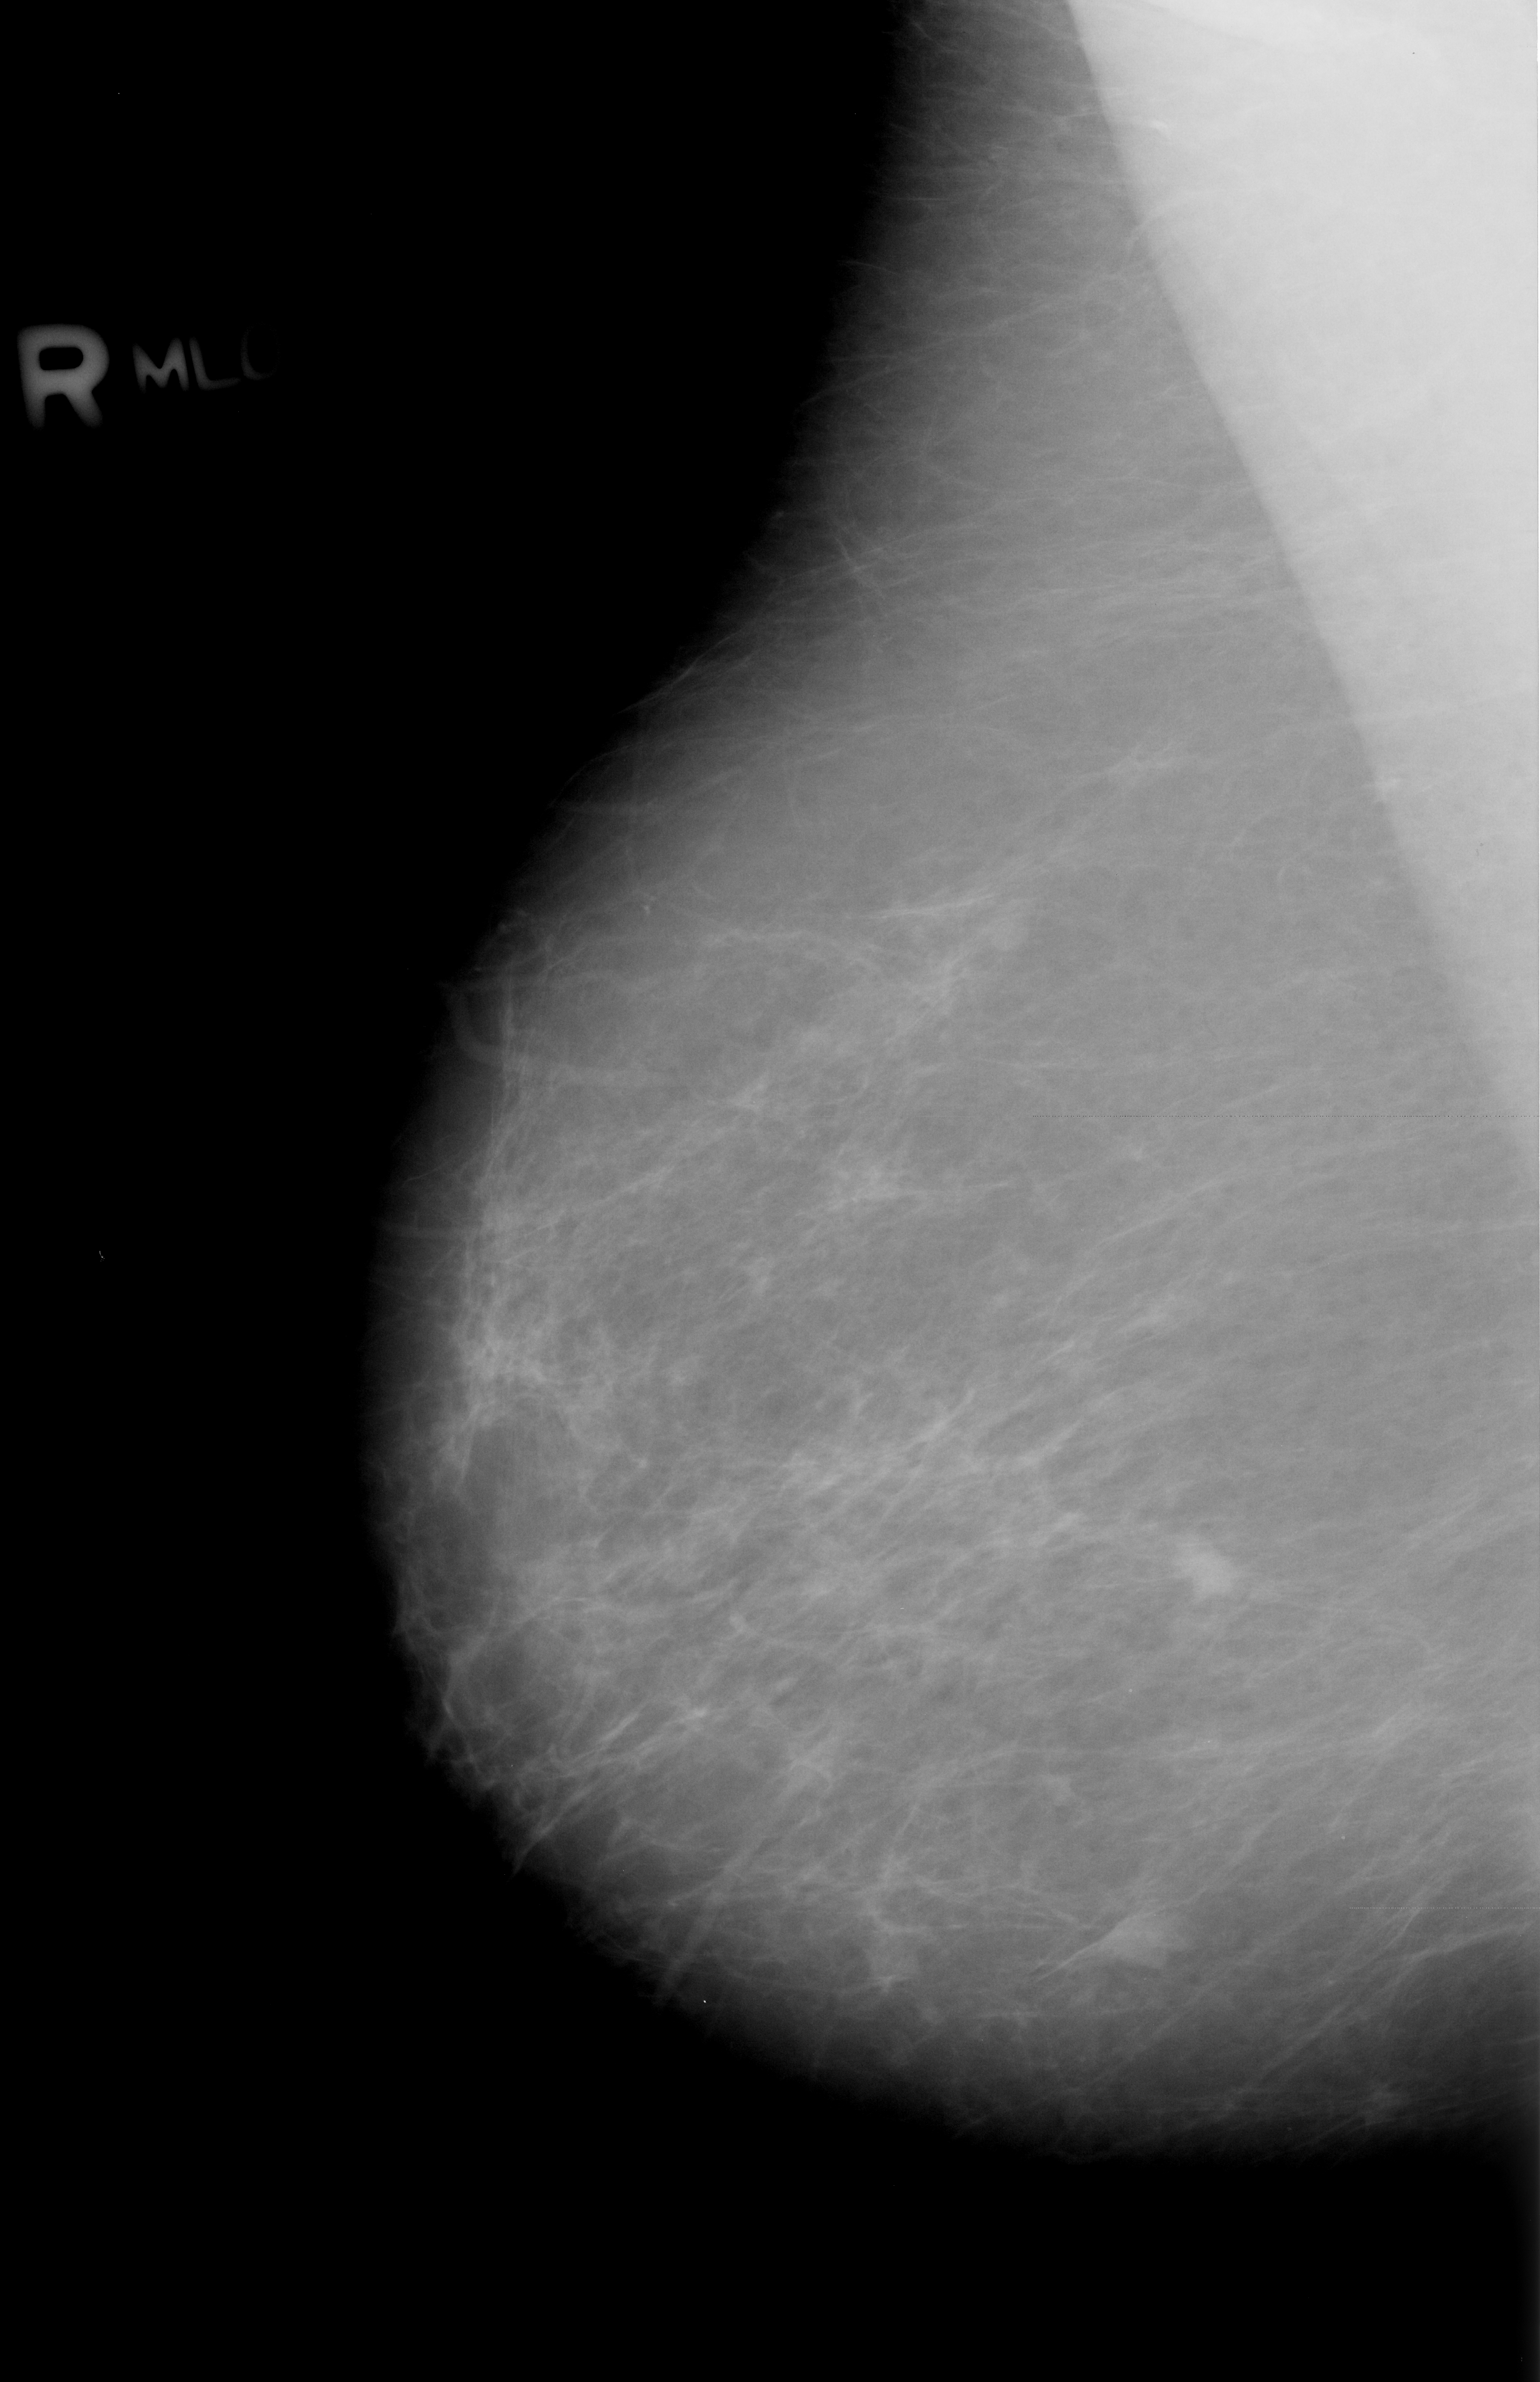
Digitized screen-film mammogram. Right breast. Mediolateral oblique (MLO) view. 1540 × 2382 image matrix.
Marked abnormalities (boxes around the expert regions of interest):
- Finding 1 of 2: mass, shape irregular, margins ill defined; BI-RADS assessment category 4; pathology result (as recorded, not read from the image): malignant: bounding box (x1, y1, x2, y2) in pixels: (1070, 1899, 1180, 1969)
- Finding 2 of 2: mass, shape irregular, margins ill defined; BI-RADS assessment category 4; subtlety rating 3 on a 1 (subtle) to 5 (obvious) scale; pathology result (as recorded, not read from the image): malignant: (1163, 1528, 1250, 1606)